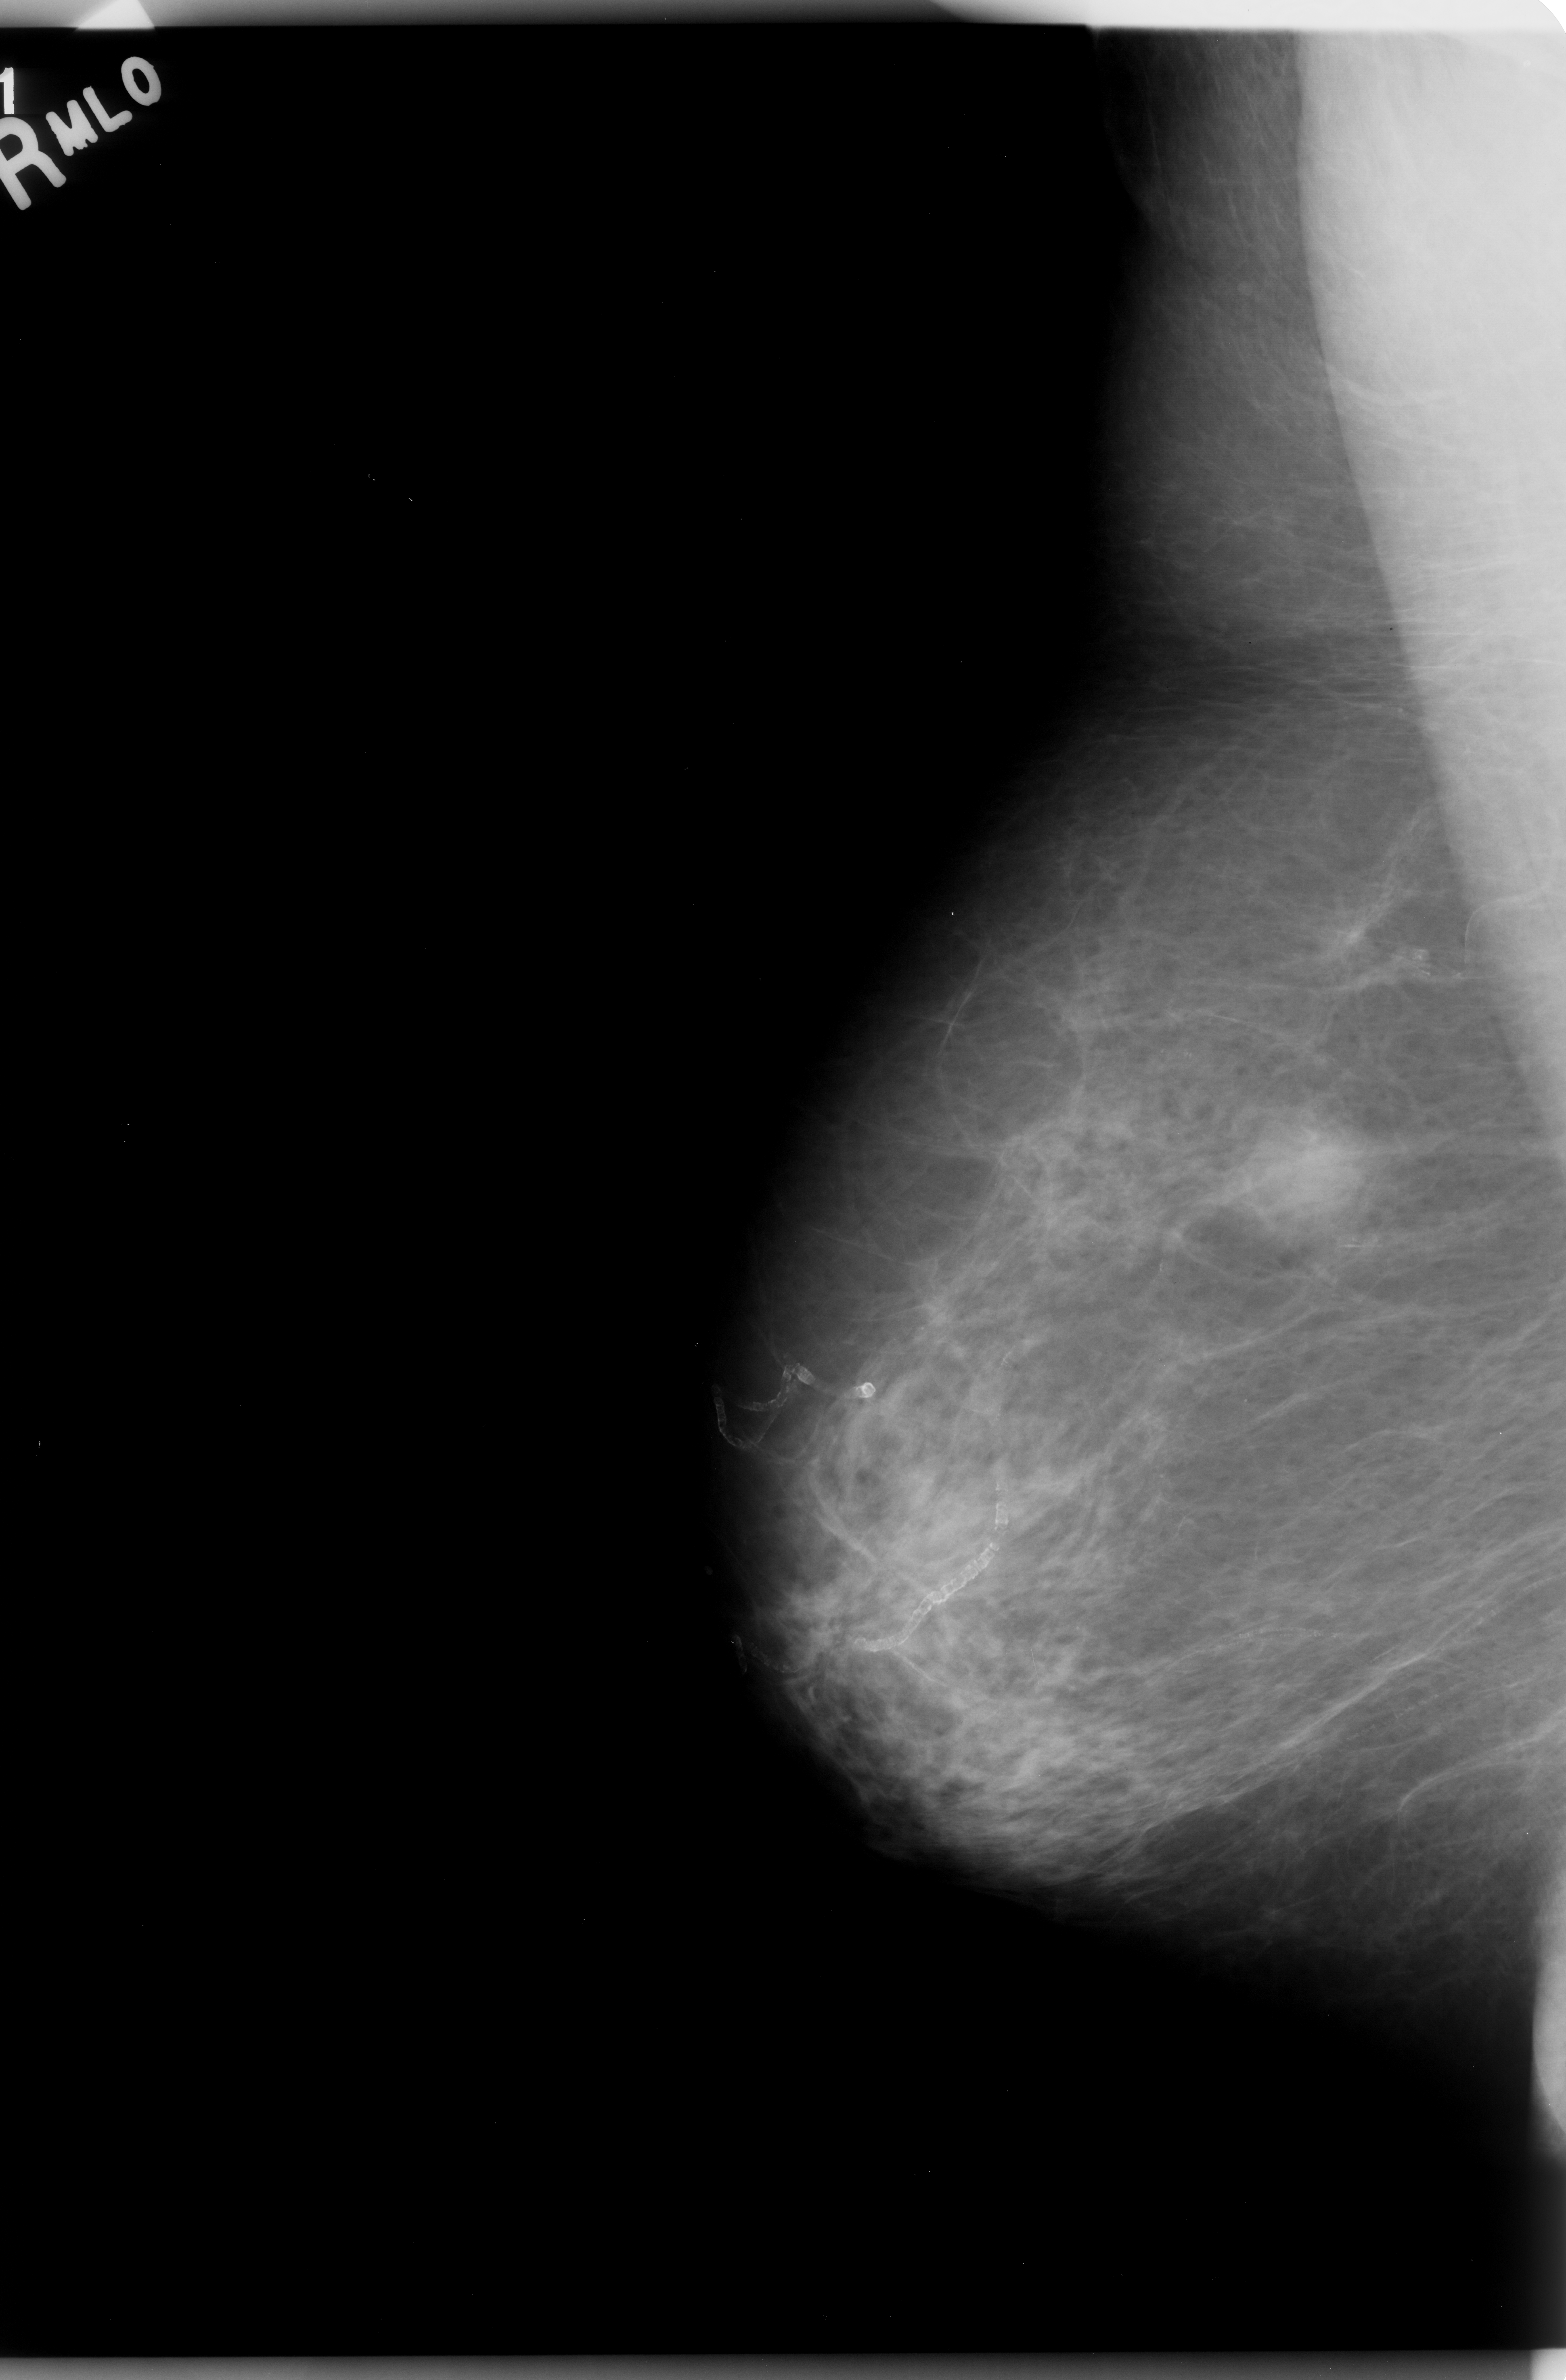
Digitized screen-film mammogram; right breast; MLO view; BI-RADS breast density category 1 (scale 1–4).
Abnormality record for this image: mass, shape round, margins ill defined; BI-RADS assessment category 5; pathology result (as recorded, not read from the image): malignant.